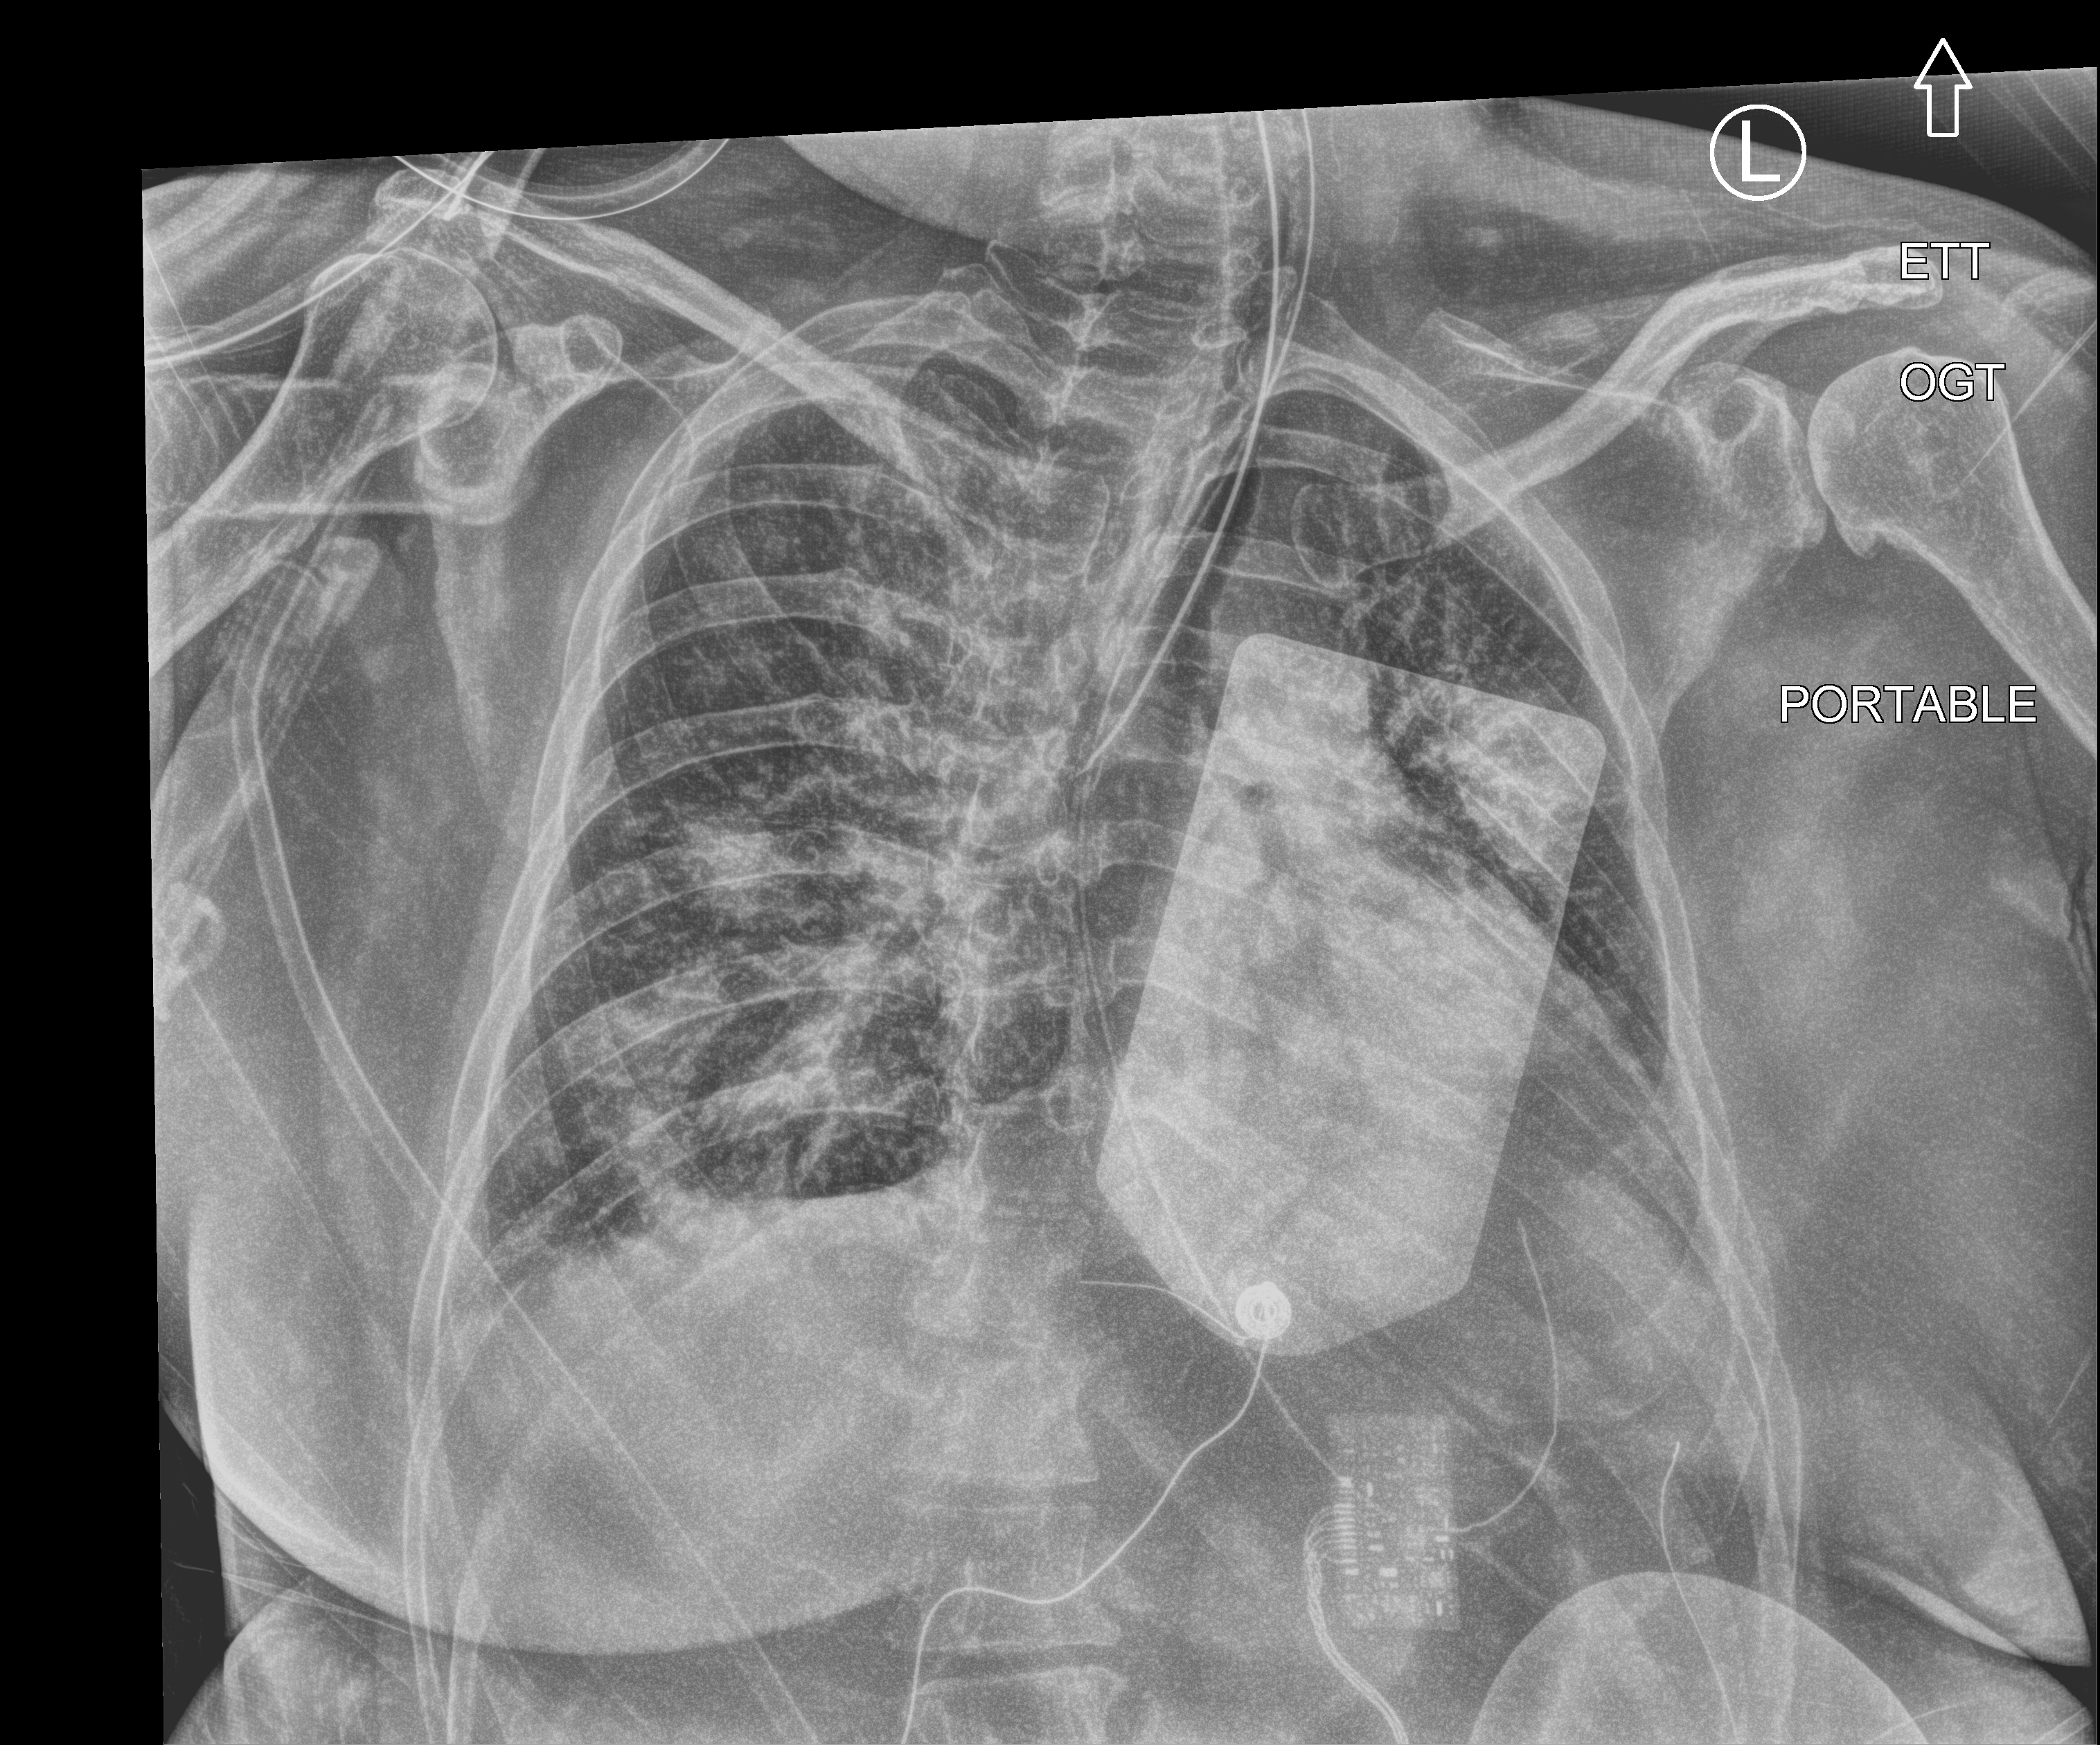
Chest X-ray (portable); anteroposterior (AP) projection. Adult patient hospitalised with COVID-19, age 18–59 years.
Admission-level facts for this patient (not findings on this image; timing relative to this image not recorded): length of hospital stay: 15 days; admitted to intensive care during this hospital stay: yes; mechanically ventilated during this hospital stay: yes.